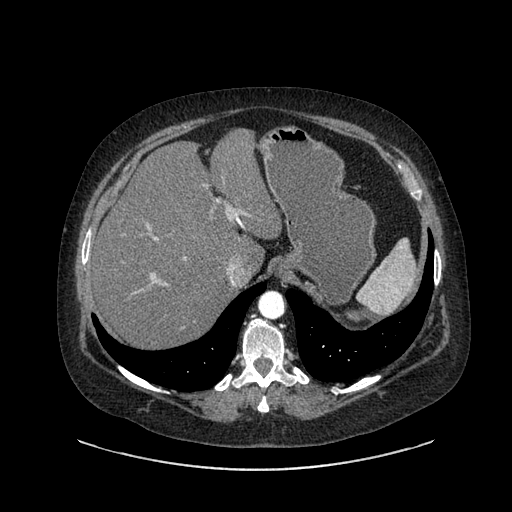
Contrast-enhanced abdominal CT, one axial slice; slice 647 of 769 in the series (ordered by position); reconstruction kernel SOFT; intravenous contrast given; soft-tissue window (W 400 / L 40 HU); 0.62 mm slice thickness; 512 × 512 image matrix, field of view 460 × 460 mm. Patient: female, 61 years. Case-level facts recorded for this patient, not image findings: diagnosis: adrenocortical carcinoma; tumour side: left adrenal; tumour size at pathology: 13 cm; Ki-67 index: 79 %.
Outlined on this slice (semi-automatic segmentation, software-assisted and operator-edited):
- mass: bounding box [x1, y1, x2, y2] px = [339, 307, 365, 328]